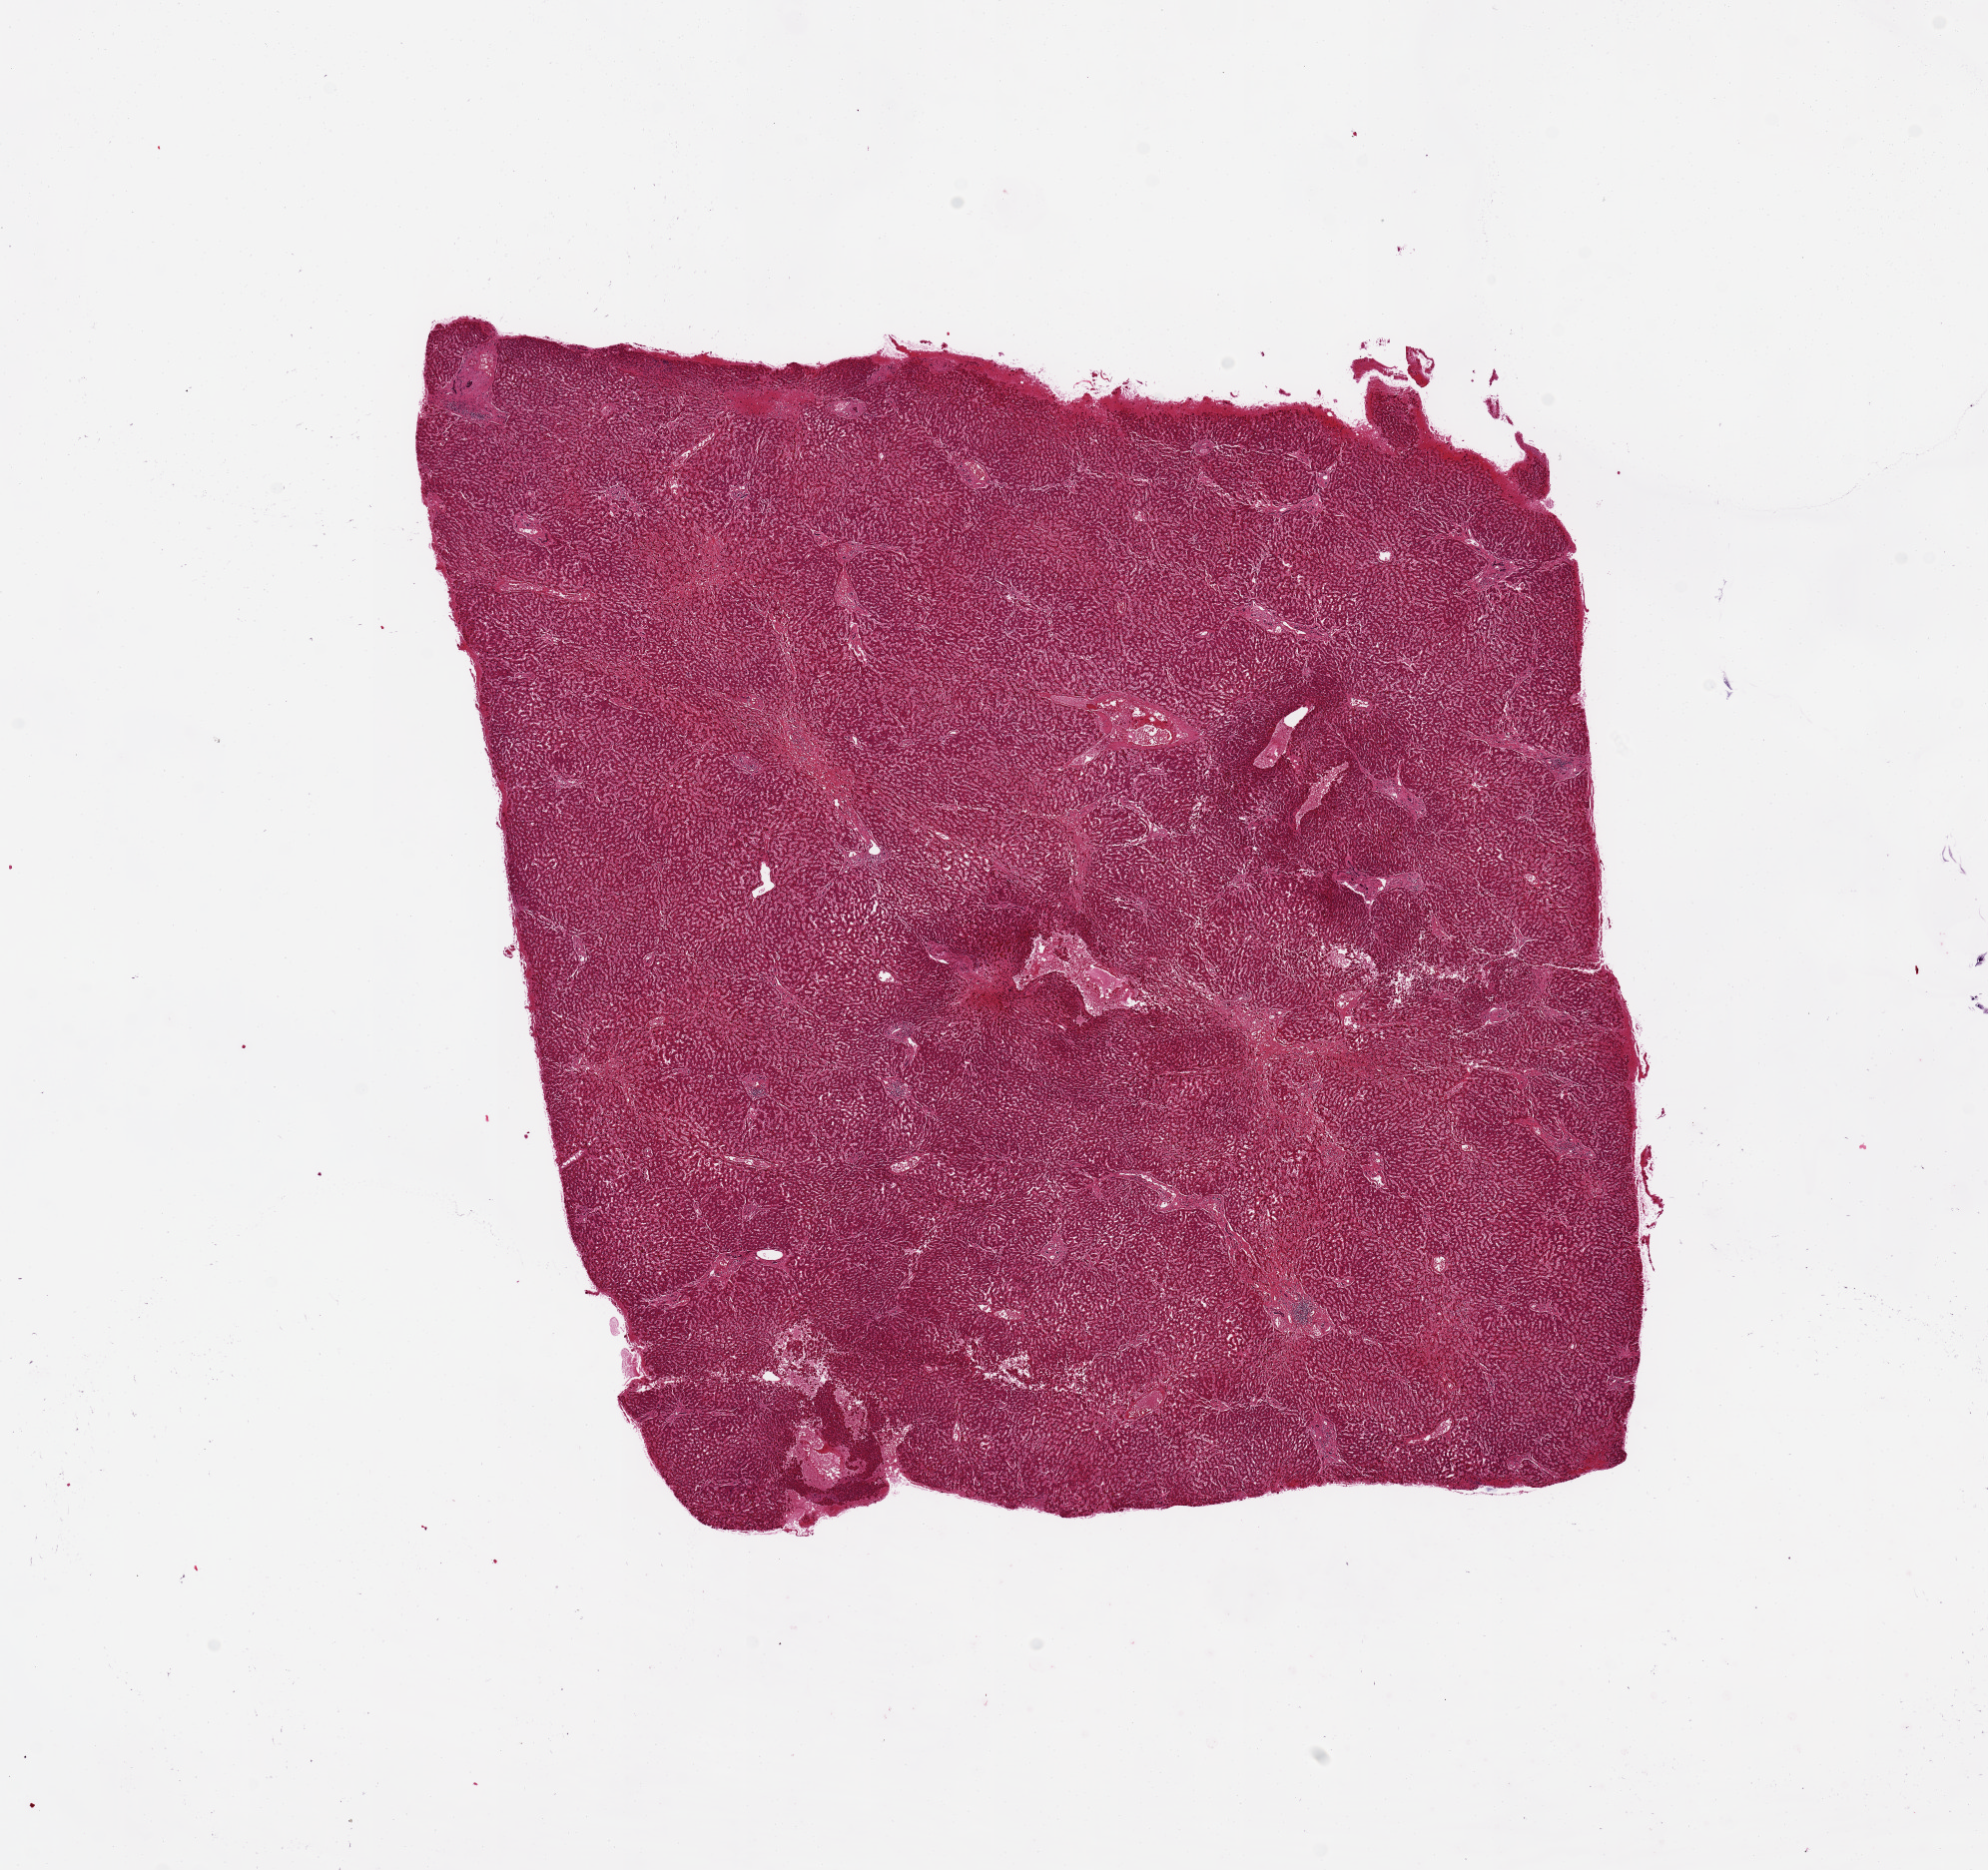
Digitized H&E-stained section, shown as a low-resolution overview of the whole scanned area (about 15.8 x 14.8 mm). PAXgene-fixed paraffin-embedded (PFPE) section. Section of liver (target tissue). Donor tissue sample. Donor: female.
- review note (as recorded): 9x9 mm